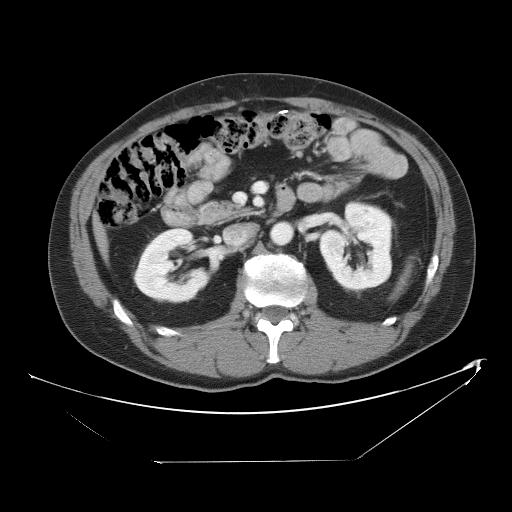
Contrast-enhanced abdominal CT, one axial slice. Position 20 of 53 along the scan axis. Reconstruction kernel STANDARD. Intravenous contrast given. Soft-tissue window (W 400 / L 40 HU). 5 mm slice thickness. 512 × 512 image matrix, field of view 438 × 438 mm. Male patient, age 59 years. Case-level facts recorded for this patient, not image findings: diagnosis: colorectal cancer liver metastases, imaged before liver resection; multiple liver metastases: yes.
Outlined on this slice (expert manual segmentation):
- planned liver remnant (the part of the liver to remain after resection): bounding box <100,232,103,241> (left, top, right, bottom; pixels)